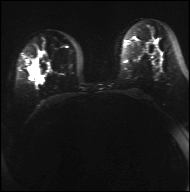
Breast MRI, one axial slice; slice 18 of 42 in the series (ordered by position); diffusion-weighted series; image 2 of 4 stored at this slice position (different b-values; order by instance number); 3 T; 4 mm slice thickness; 190 × 192 image matrix, field of view 317 × 320 mm. Female patient.
Annotated regions visible in this slice (outlined manually by an expert reader):
- tumour on diffusion-weighted imaging: bounding box [x1, y1, x2, y2] px = [75, 64, 99, 76]